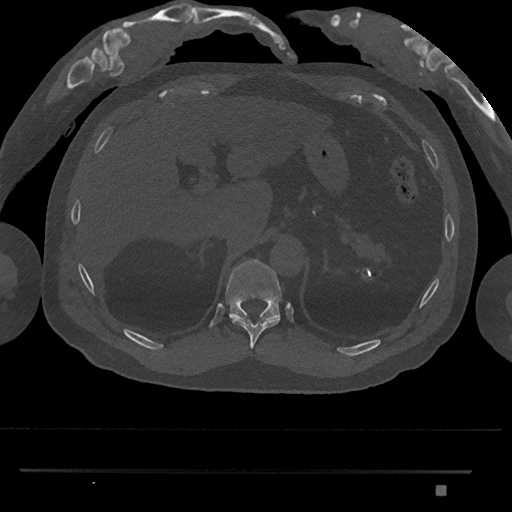
CT including the spine, one axial slice. Slice 973 of 1134 in the series (ordered by position). Reconstruction kernel Br40s/3. Bone window (W 1800 / L 400 HU). 0.5 mm slice thickness. 512 × 512 image matrix. Male patient, age 65 years. Case-level facts recorded for this patient, not image findings: primary cancer: prostate.
Structures marked on this image (semi-automatically segmented with operator editing):
- T10 vertebra: bounding box [x1, y1, x2, y2] px = [231, 317, 280, 349]
- T11 vertebra: [225, 259, 283, 320]